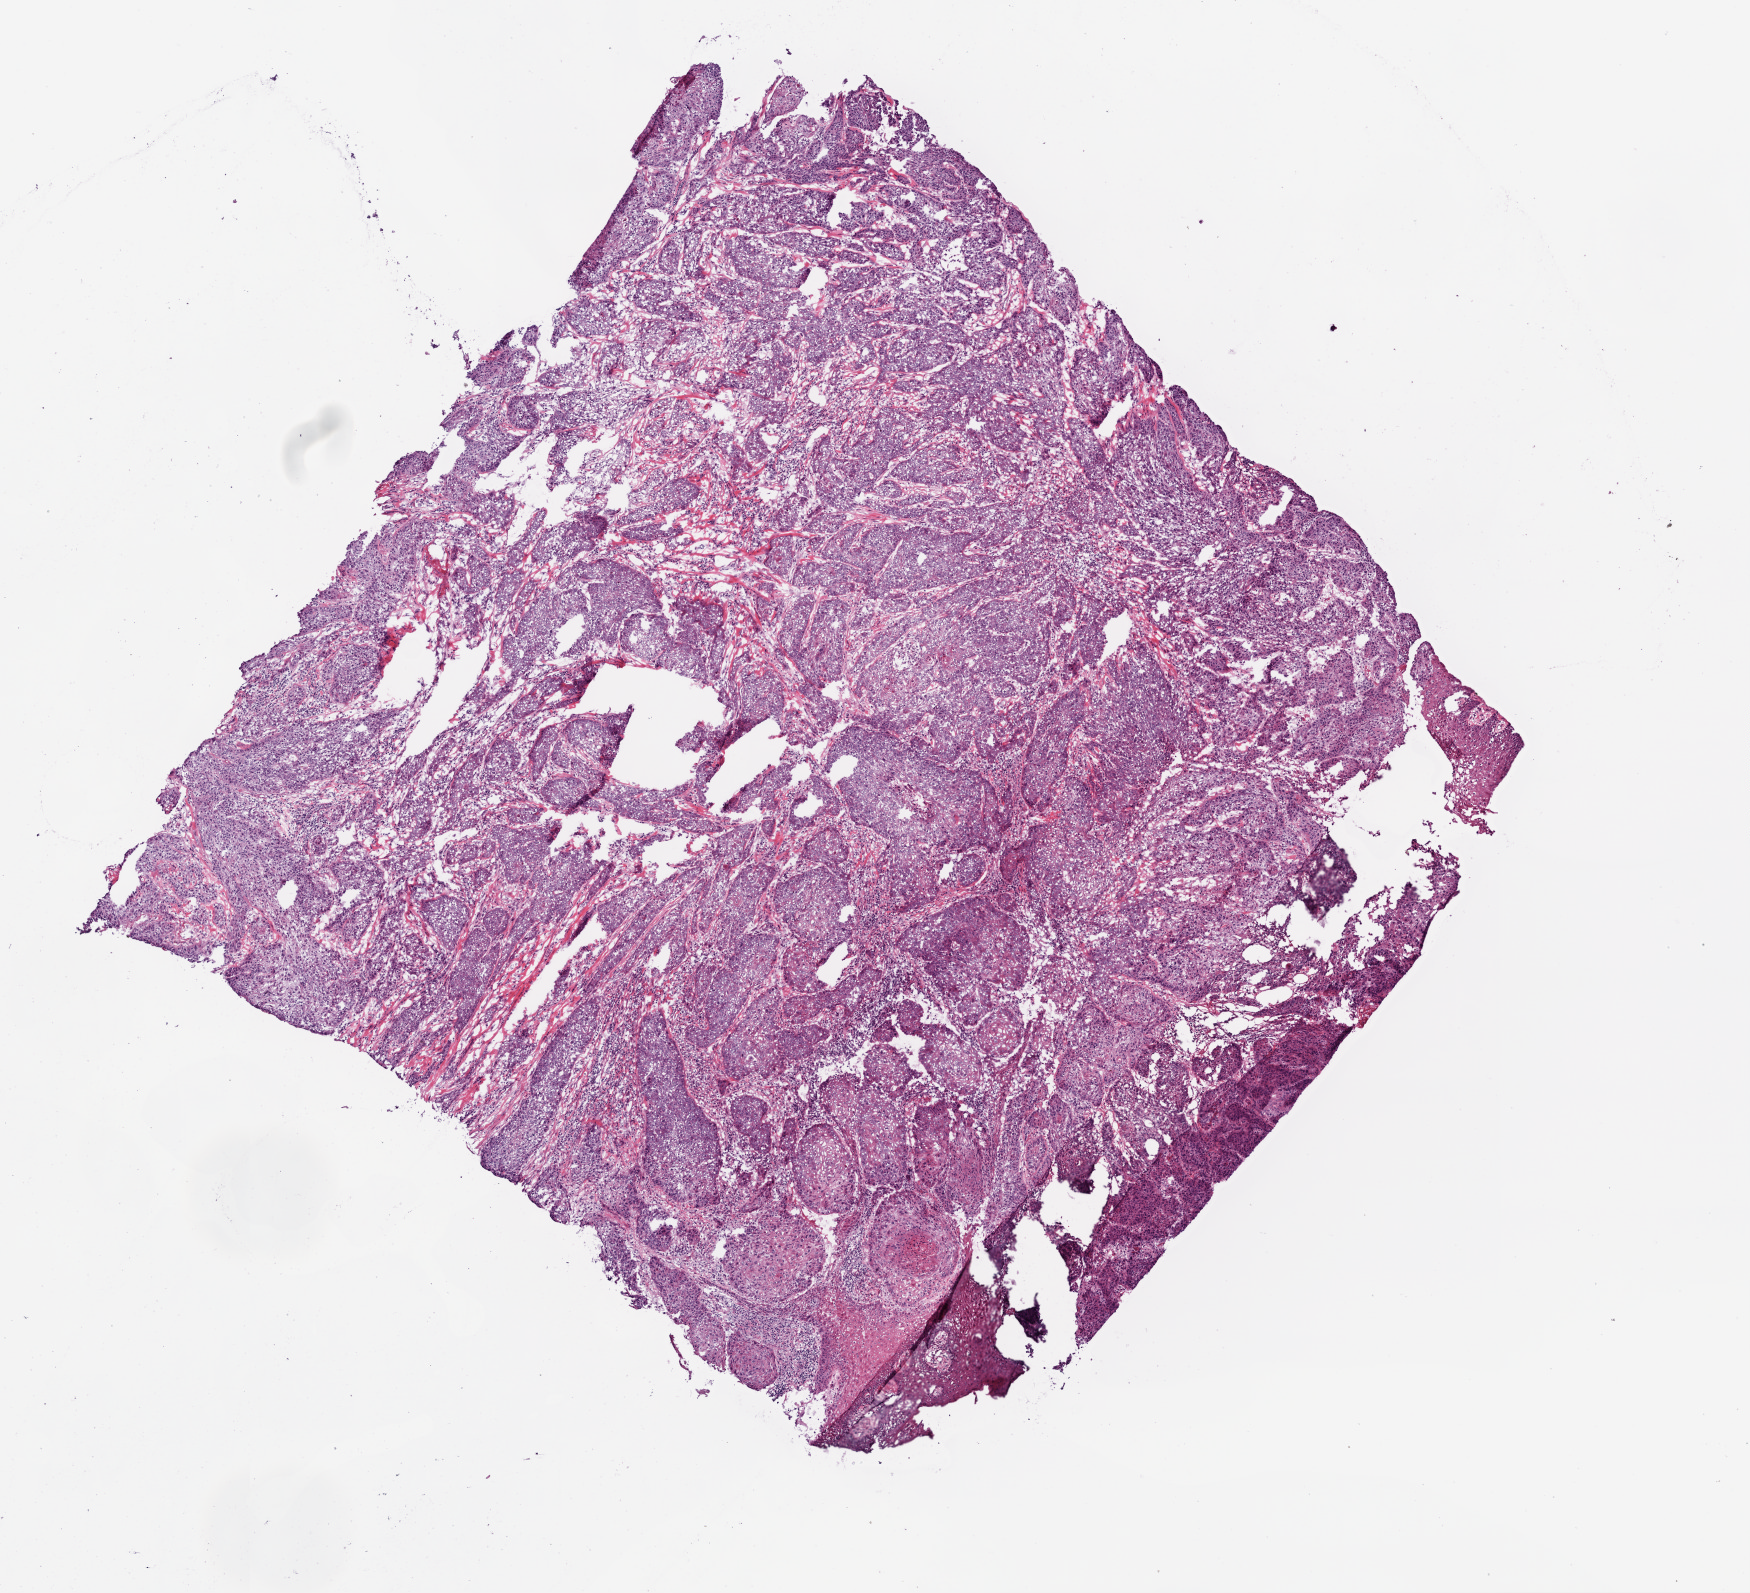
Whole-slide histology image, Hematoxylin and eosin (H&E) stained, a low-resolution overview of the entire scanned area, about 7.0 x 6.4 mm (from a 20x scan); frozen section; primary tumour sample from the head and neck. Female patient; age at initial diagnosis 45 years. Histologic grade: G2 (moderately differentiated). Composition of this section per pathologist review: tumour cells 85%, tumour nuclei 85%, normal cells 0%, stromal cells 10%, necrosis 5%.
* AJCC pathologic stage: IVA (6th edition)
* histologic diagnosis: Squamous cell carcinoma, NOS (tongue, NOS)